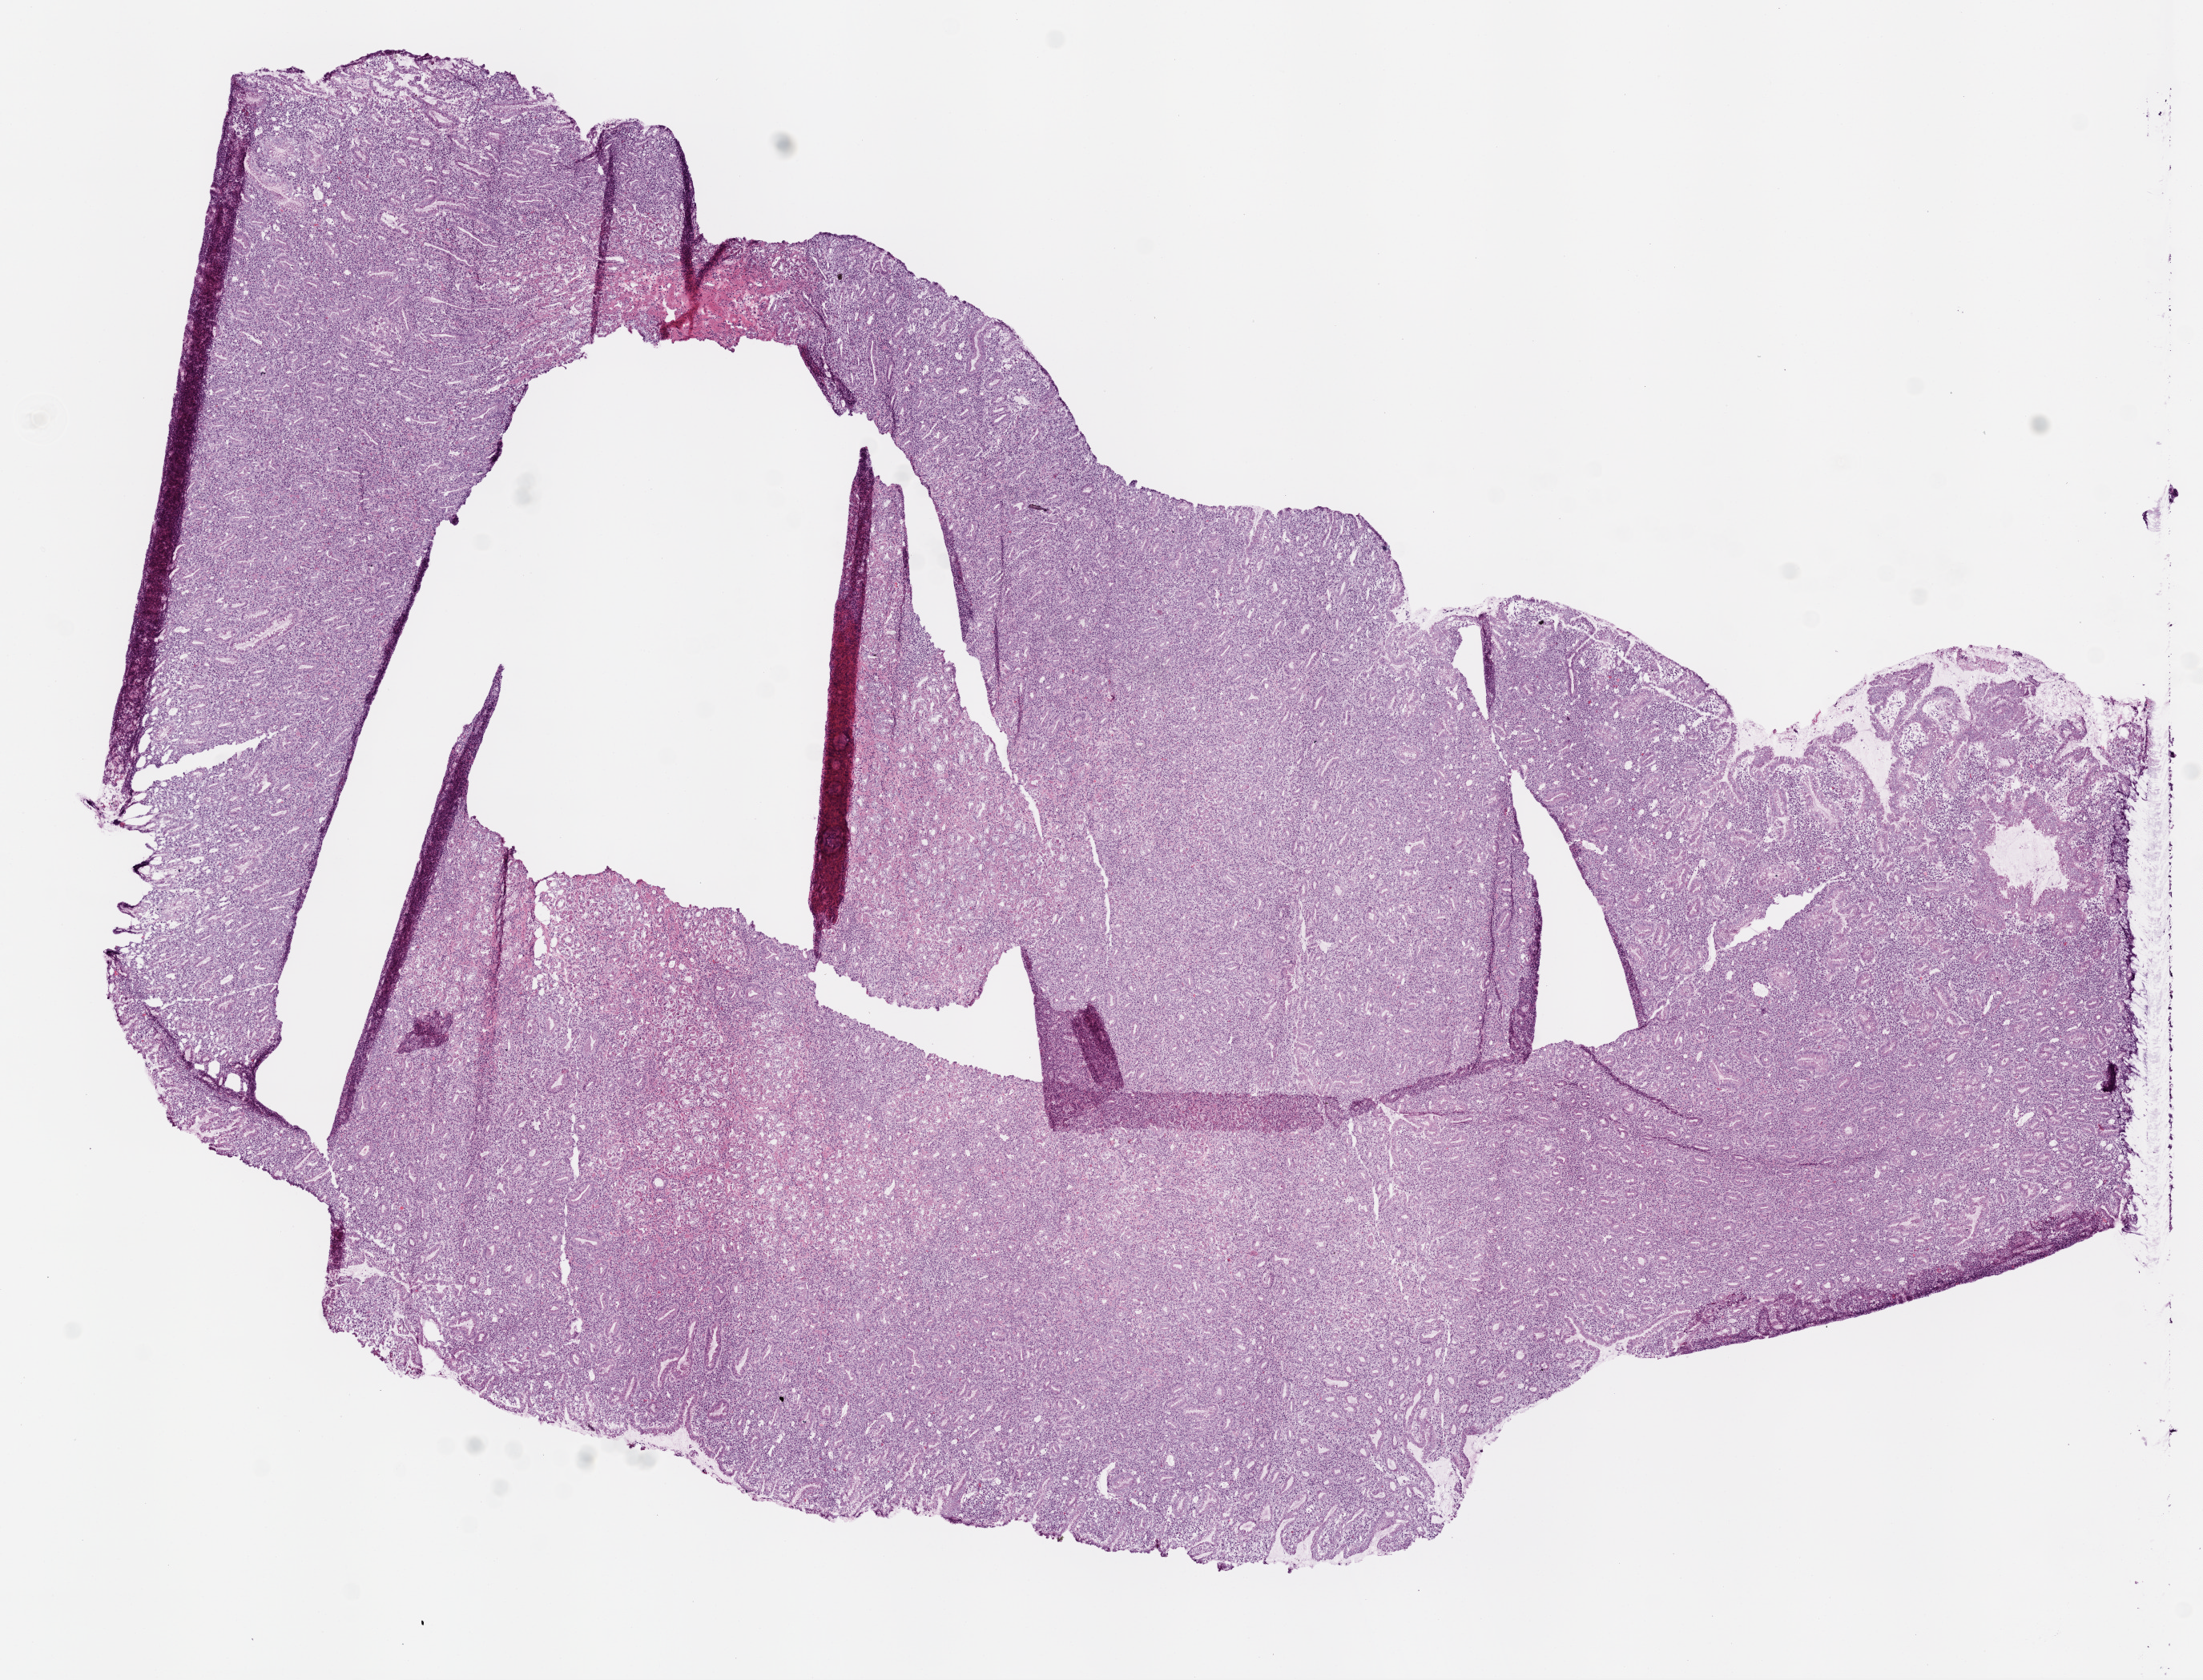
Hematoxylin and eosin (H&E) stained whole-slide image — low-resolution overview of the scanned area, about 11.0 x 8.4 mm (from a 20x scan); frozen section from the top of the tissue portion; sample: solid tissue normal (non-tumour tissue), stomach. Patient: female, age at initial diagnosis 66 years.
This section: solid tissue normal (non-tumour) sample from the same patient. Patient diagnosis: Adenocarcinoma, NOS (cardia, NOS).